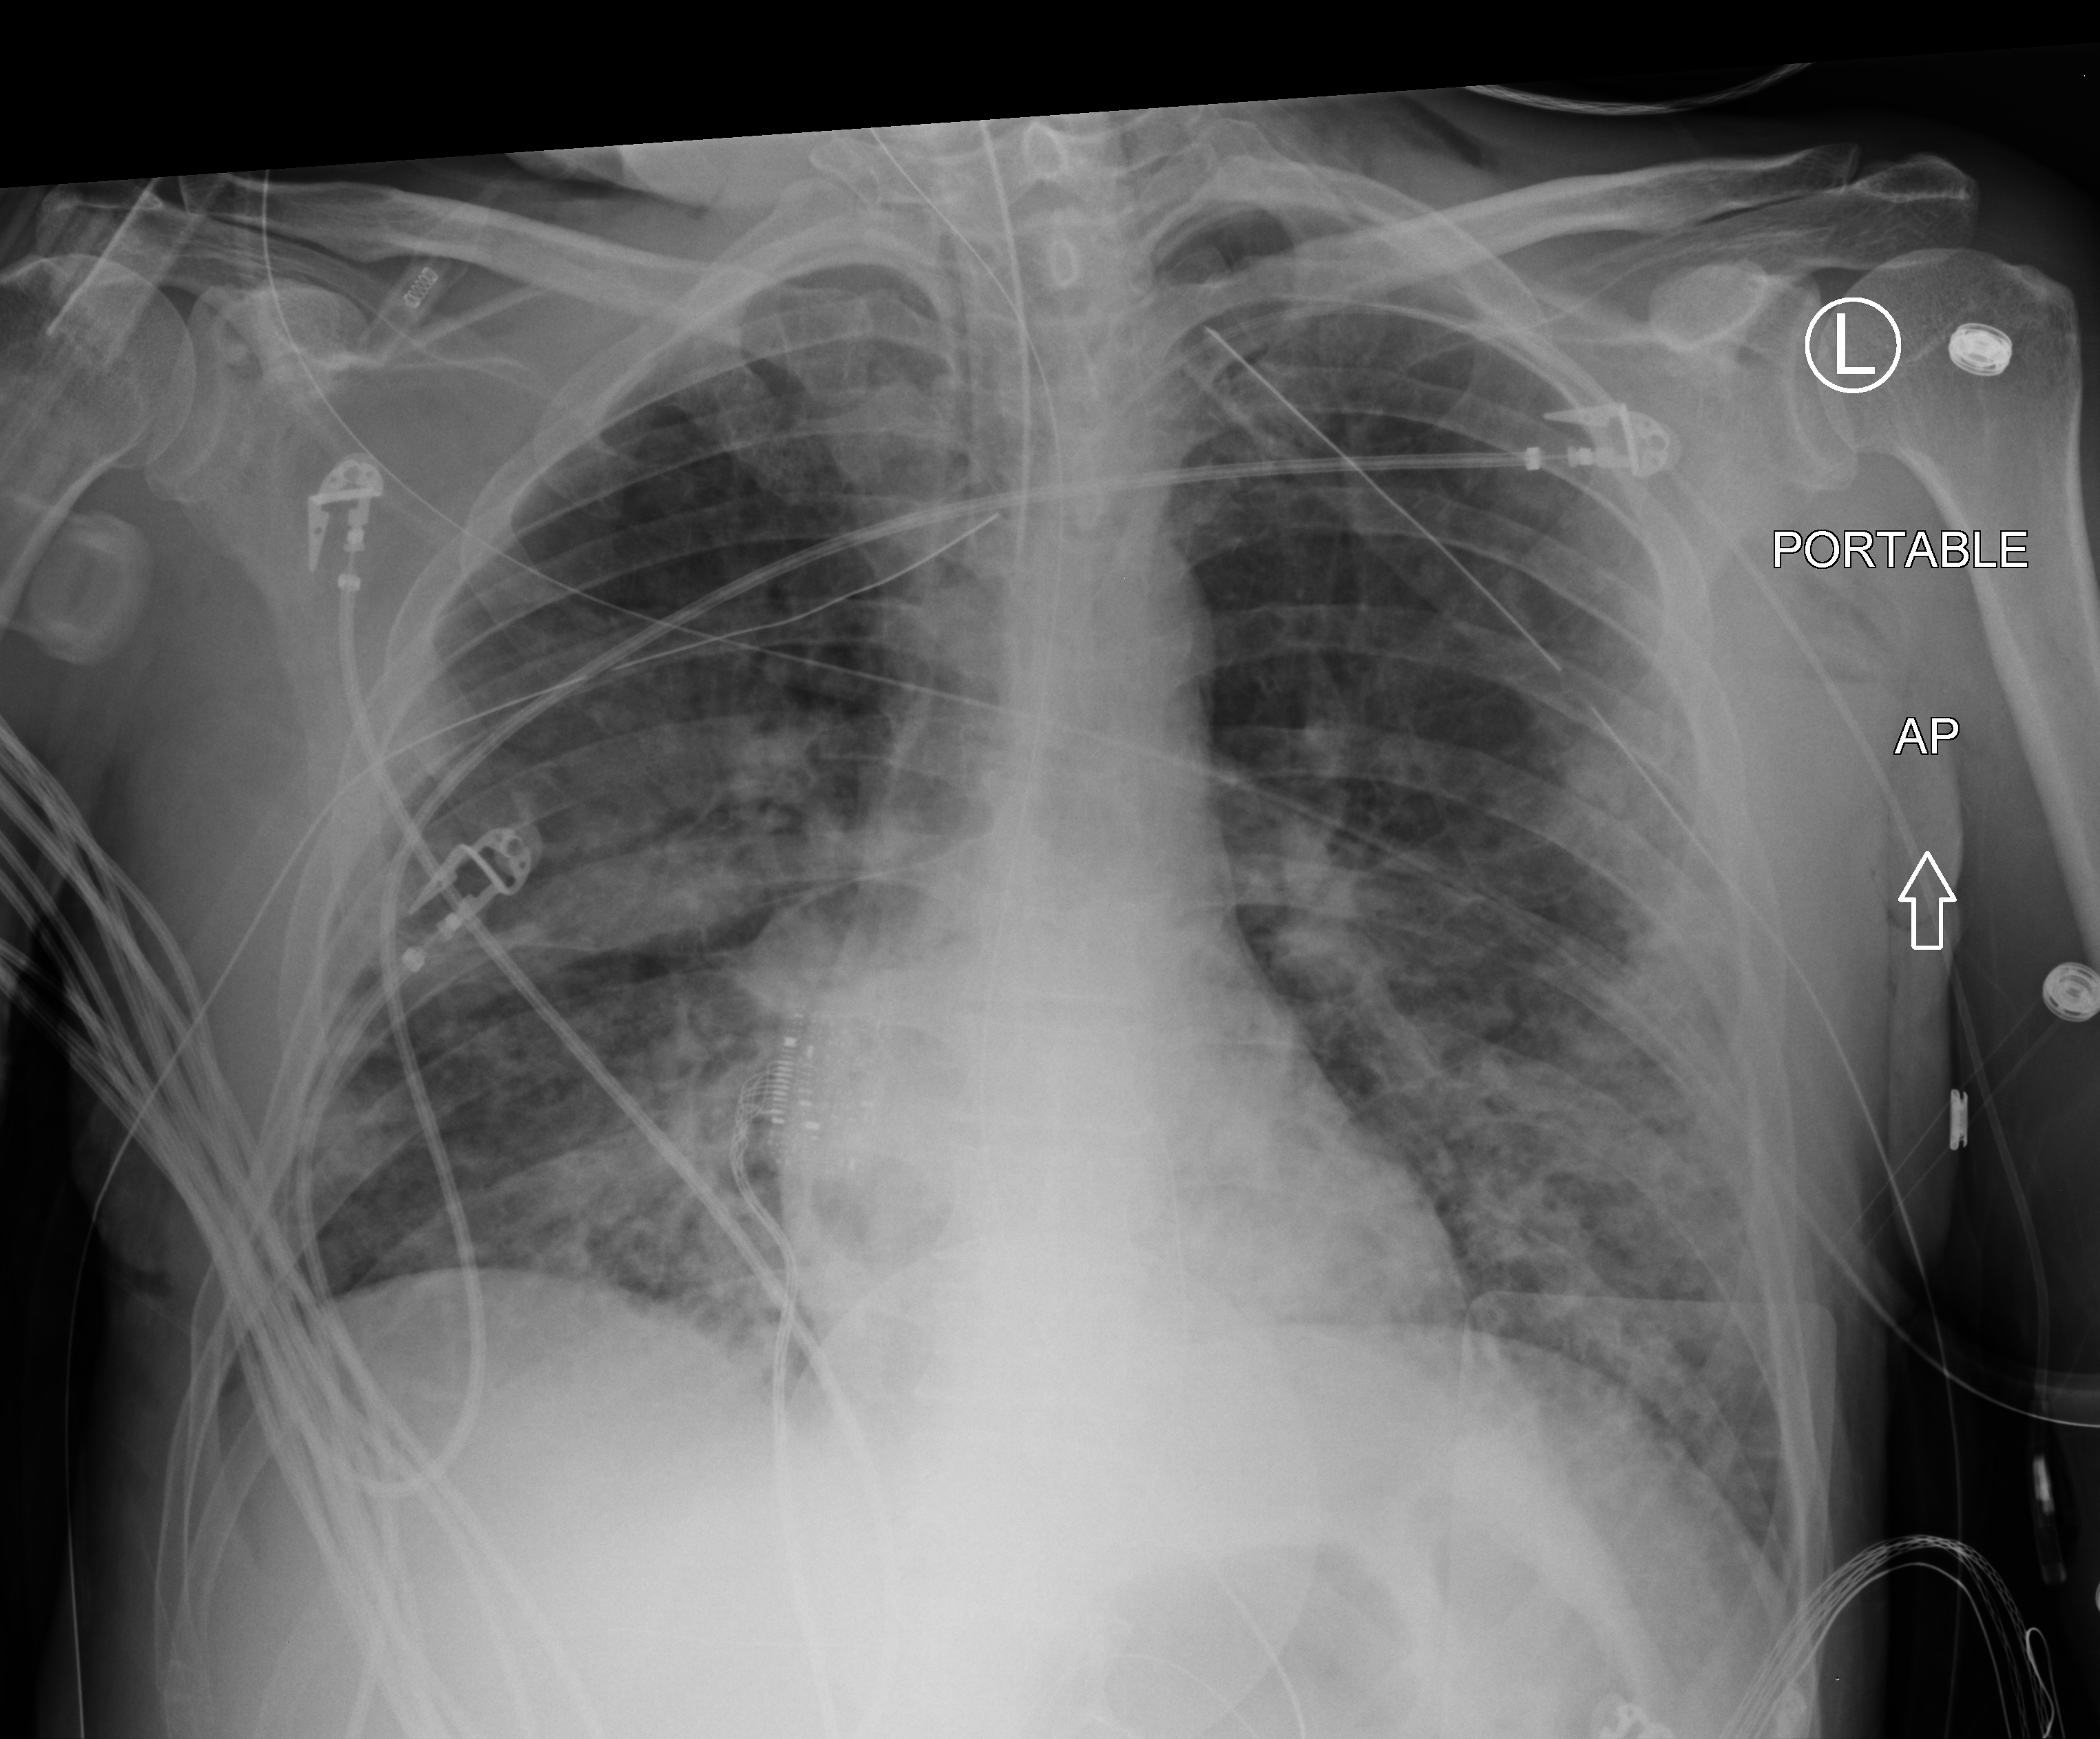
Chest X-ray (portable); anteroposterior (AP) projection. Male patient hospitalised with COVID-19, age 18–59 years.
Hospital-stay facts (about this admission, not read from this image; timing relative to this image not recorded): admitted to intensive care during this hospital stay: yes.